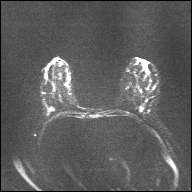
Breast MRI, one axial slice. Slice 17 of 32 in the series (ordered by position). Diffusion-weighted series; image 2 of 4 stored at this slice position (different b-values; order by instance number). 1.5 T. 192 × 192 image matrix, field of view 360 × 360 mm. Female patient.
Outlined on this slice (outlined manually by an expert reader):
- tumour on diffusion-weighted imaging: bounding box <48,108,54,111> (left, top, right, bottom; pixels)